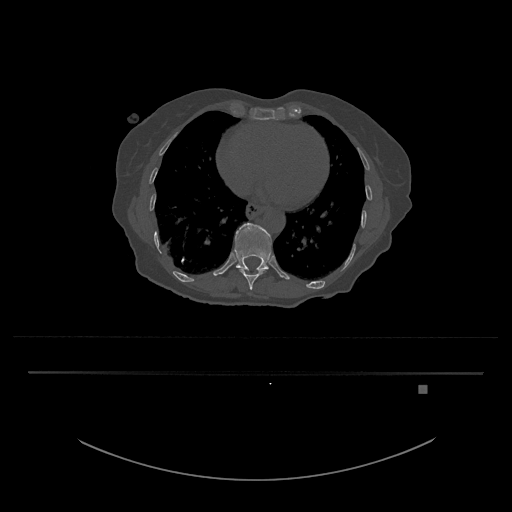
CT including the spine, one axial slice; slice 689 of 797 in the series (ordered by position); 120 kVp; bone window (W 1800 / L 400 HU); 0.5 mm slice thickness; 512 × 512 image matrix. Female patient, age 57 years. Case-level facts recorded for this patient, not image findings: primary cancer: cervical.
Outlined on this slice (semi-automatic segmentation, software-assisted and operator-edited):
- T10 vertebra: bounding box <239,268,267,290> (left, top, right, bottom; pixels)
- T11 vertebra: <234,223,272,271>